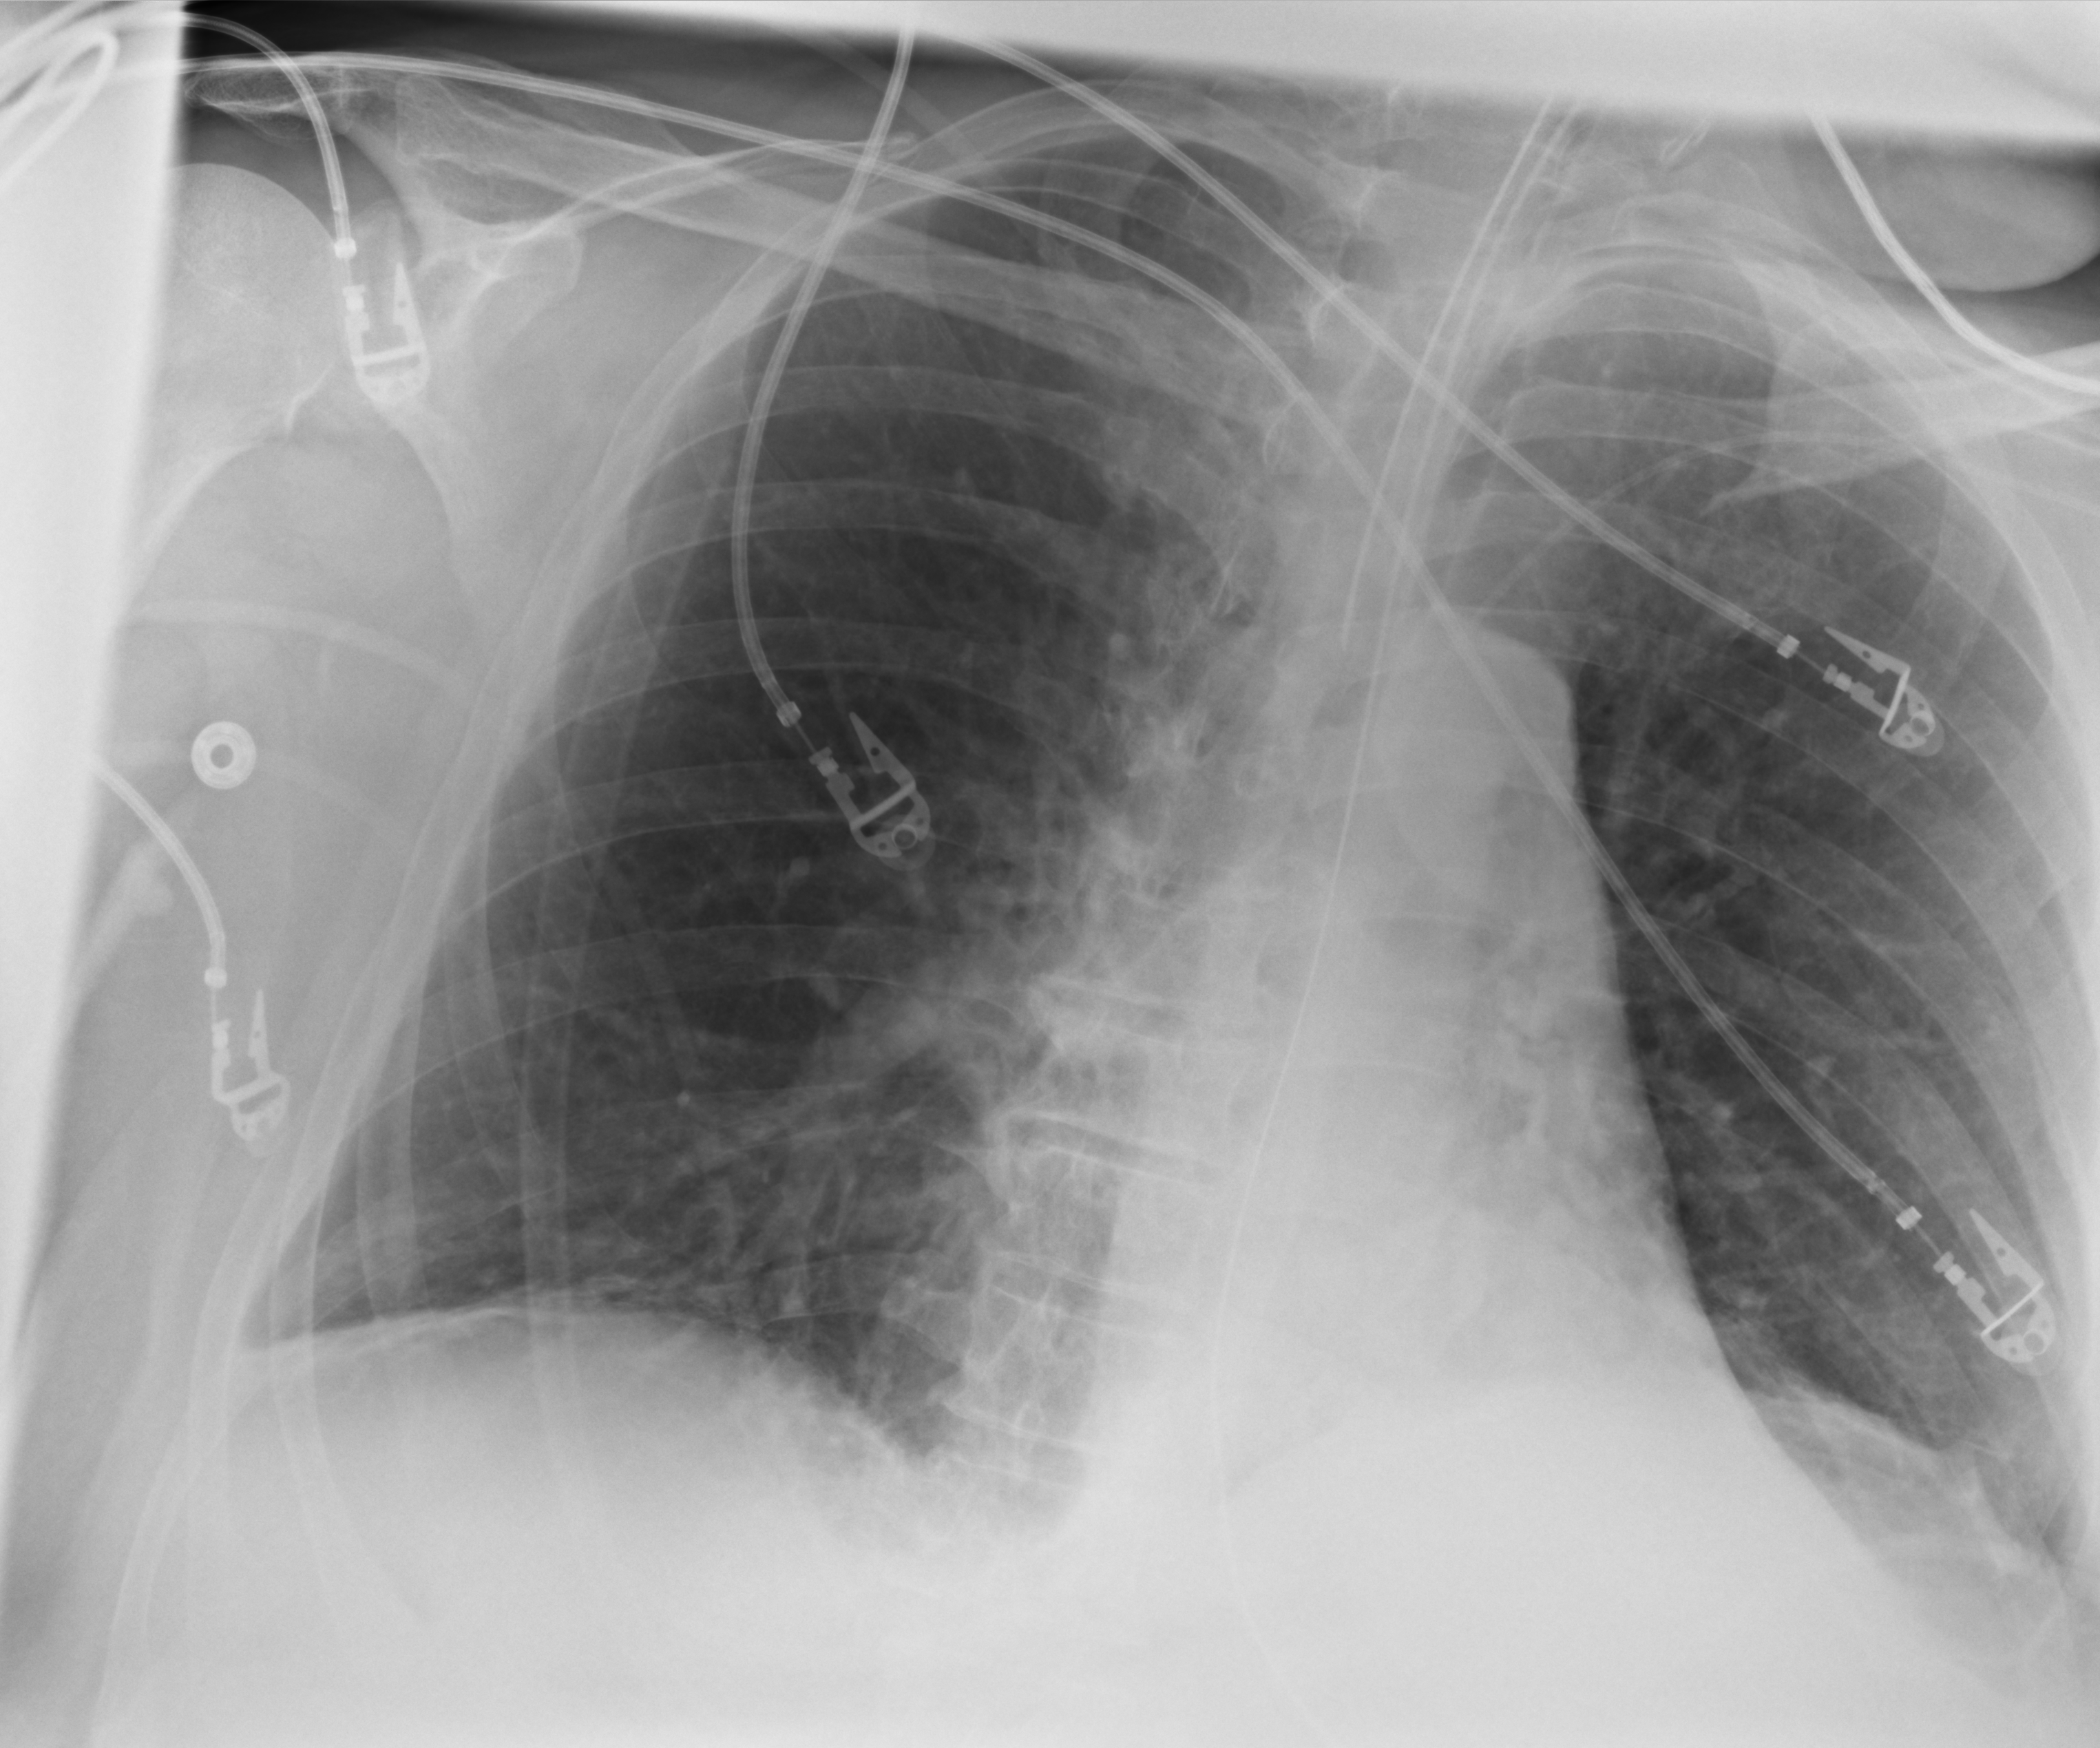
Bedside chest radiograph (computed radiography), anteroposterior (AP) projection. Patient hospitalised with COVID-19; male, aged 60–74 years.
From the hospital-stay record, not from the radiograph (when in the stay this image was taken is not recorded): admitted to intensive care during this hospital stay: yes; other chronic lung disease (admission record): no.